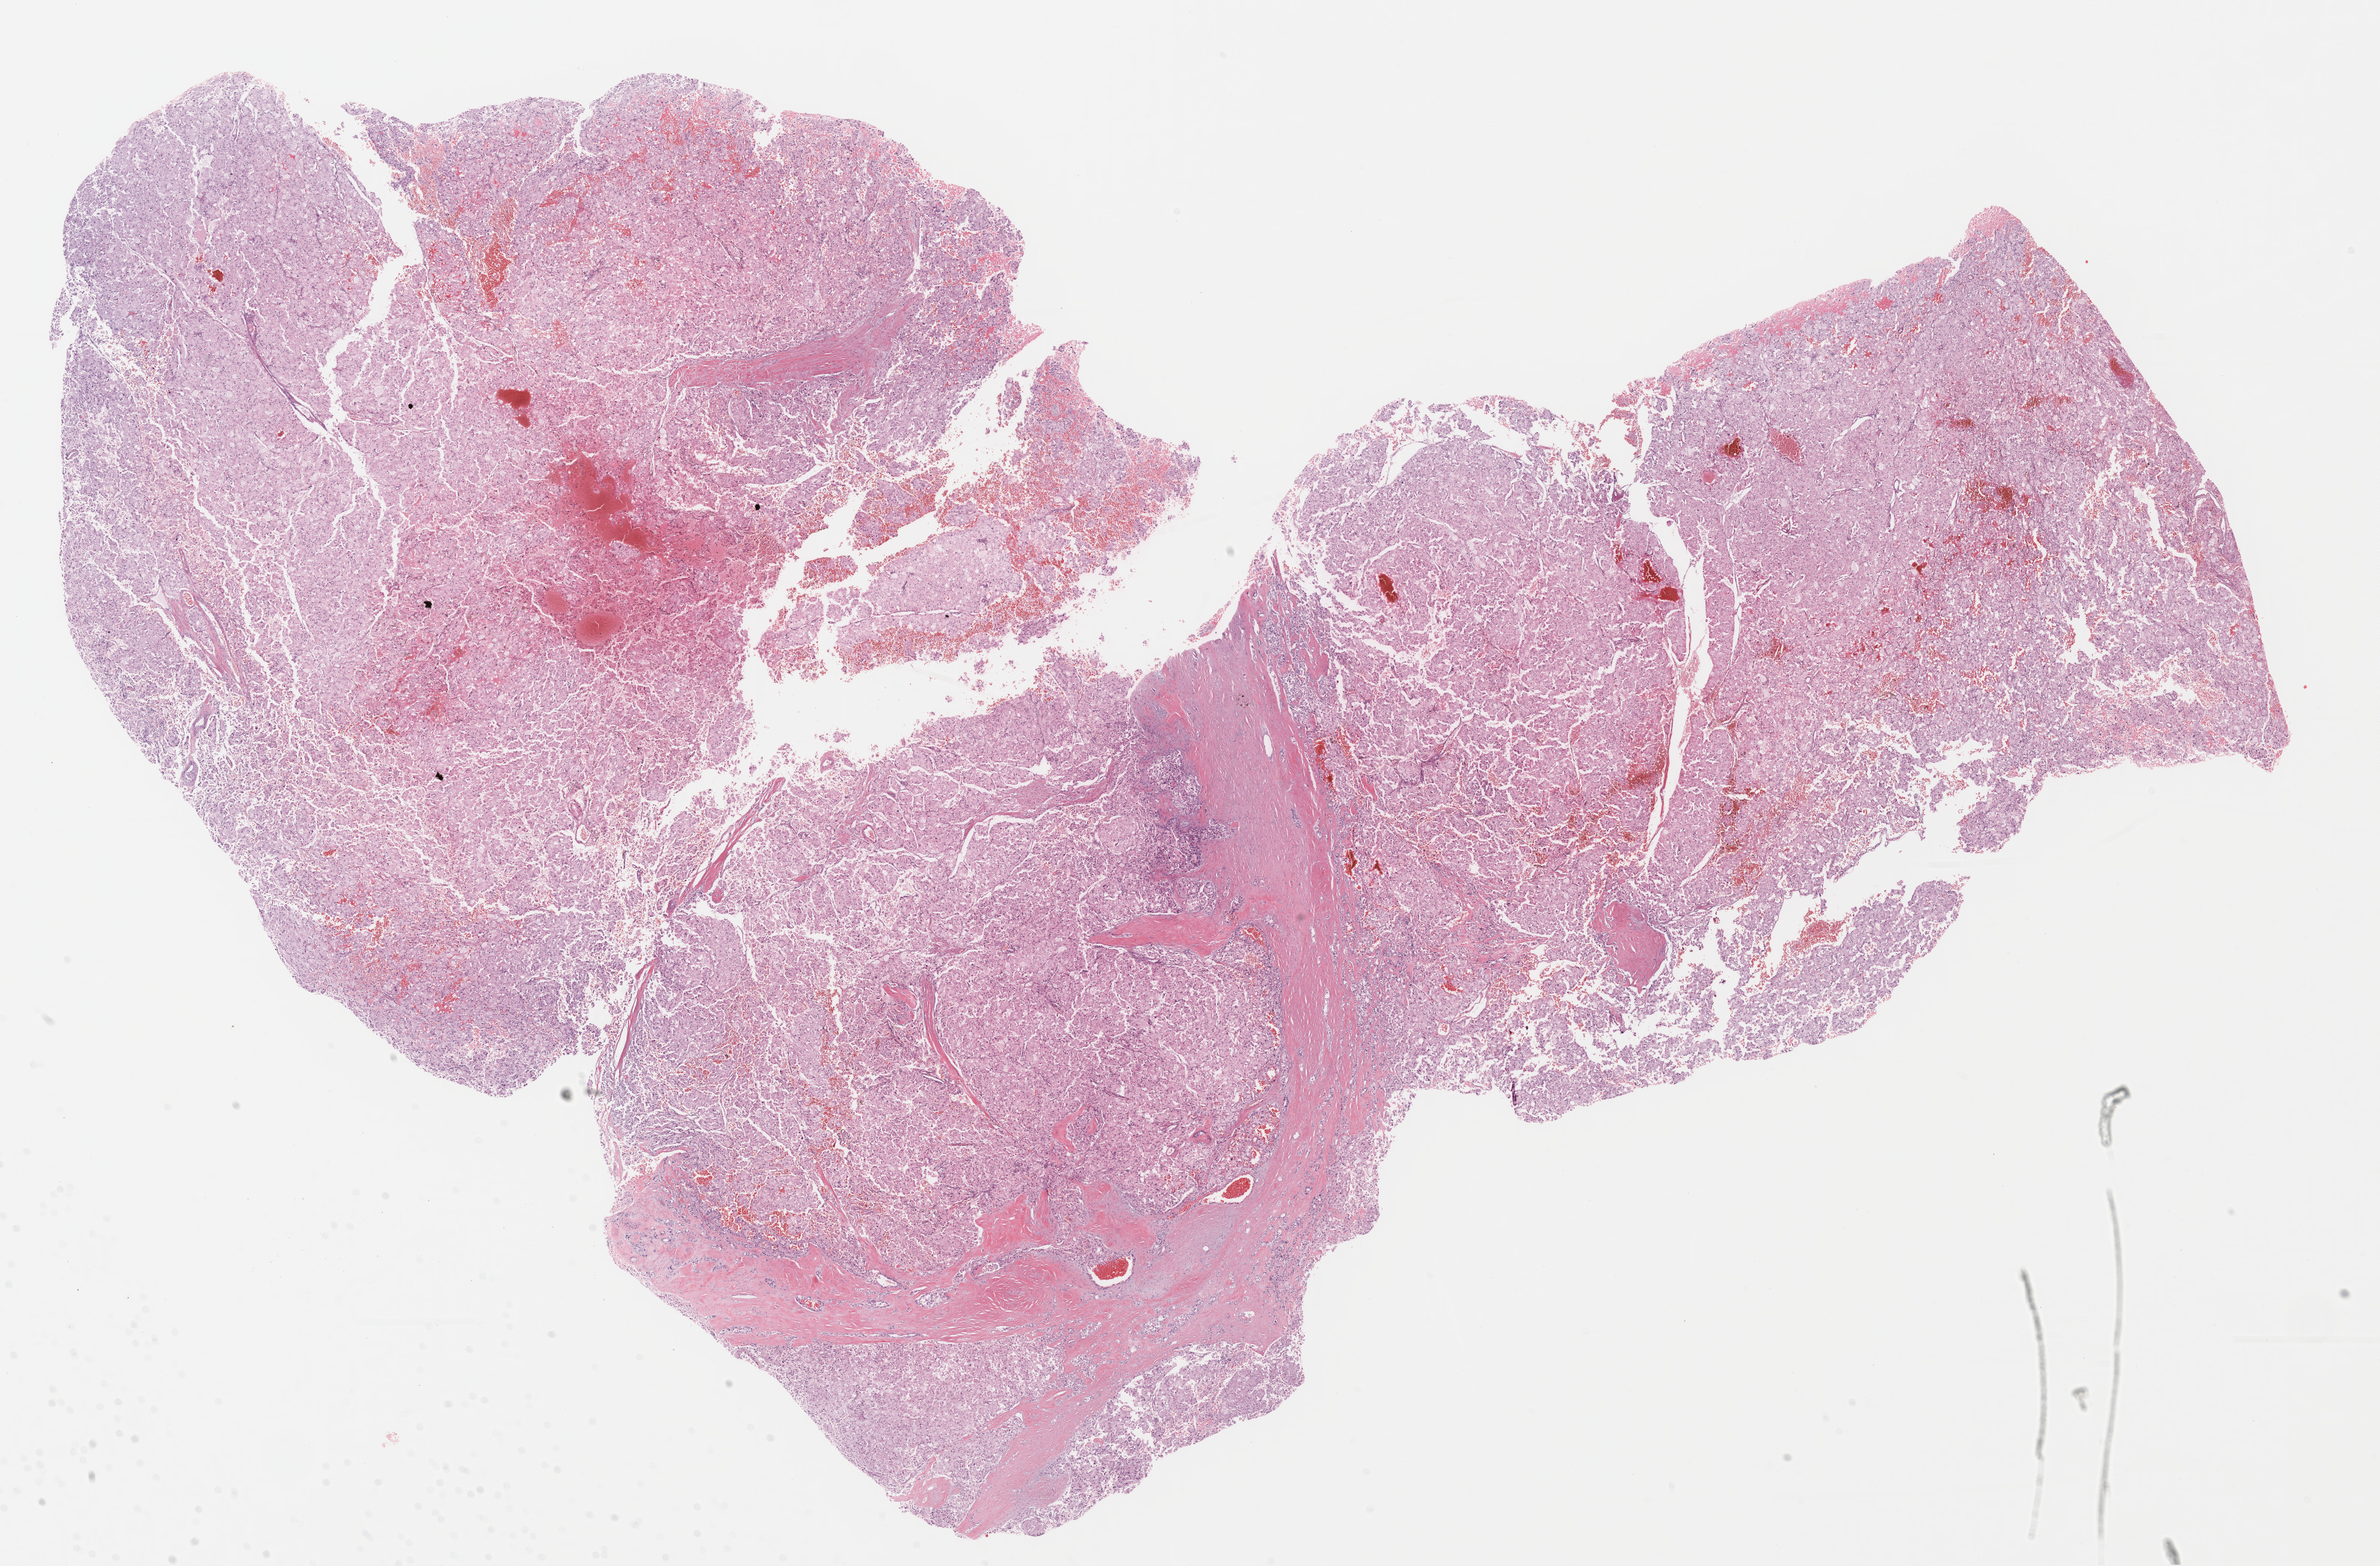
Digitized H&E-stained tissue section (whole slide), low-resolution overview of the scanned area, about 25.0 x 16.5 mm; FFPE section; sample: primary tumour, kidney. Patient: female, age at initial diagnosis 44 years.
Laterality: right. AJCC pathologic stage: I (7th edition). Diagnosis: Renal cell carcinoma, chromophobe type. TNM: T1 N0 M0.